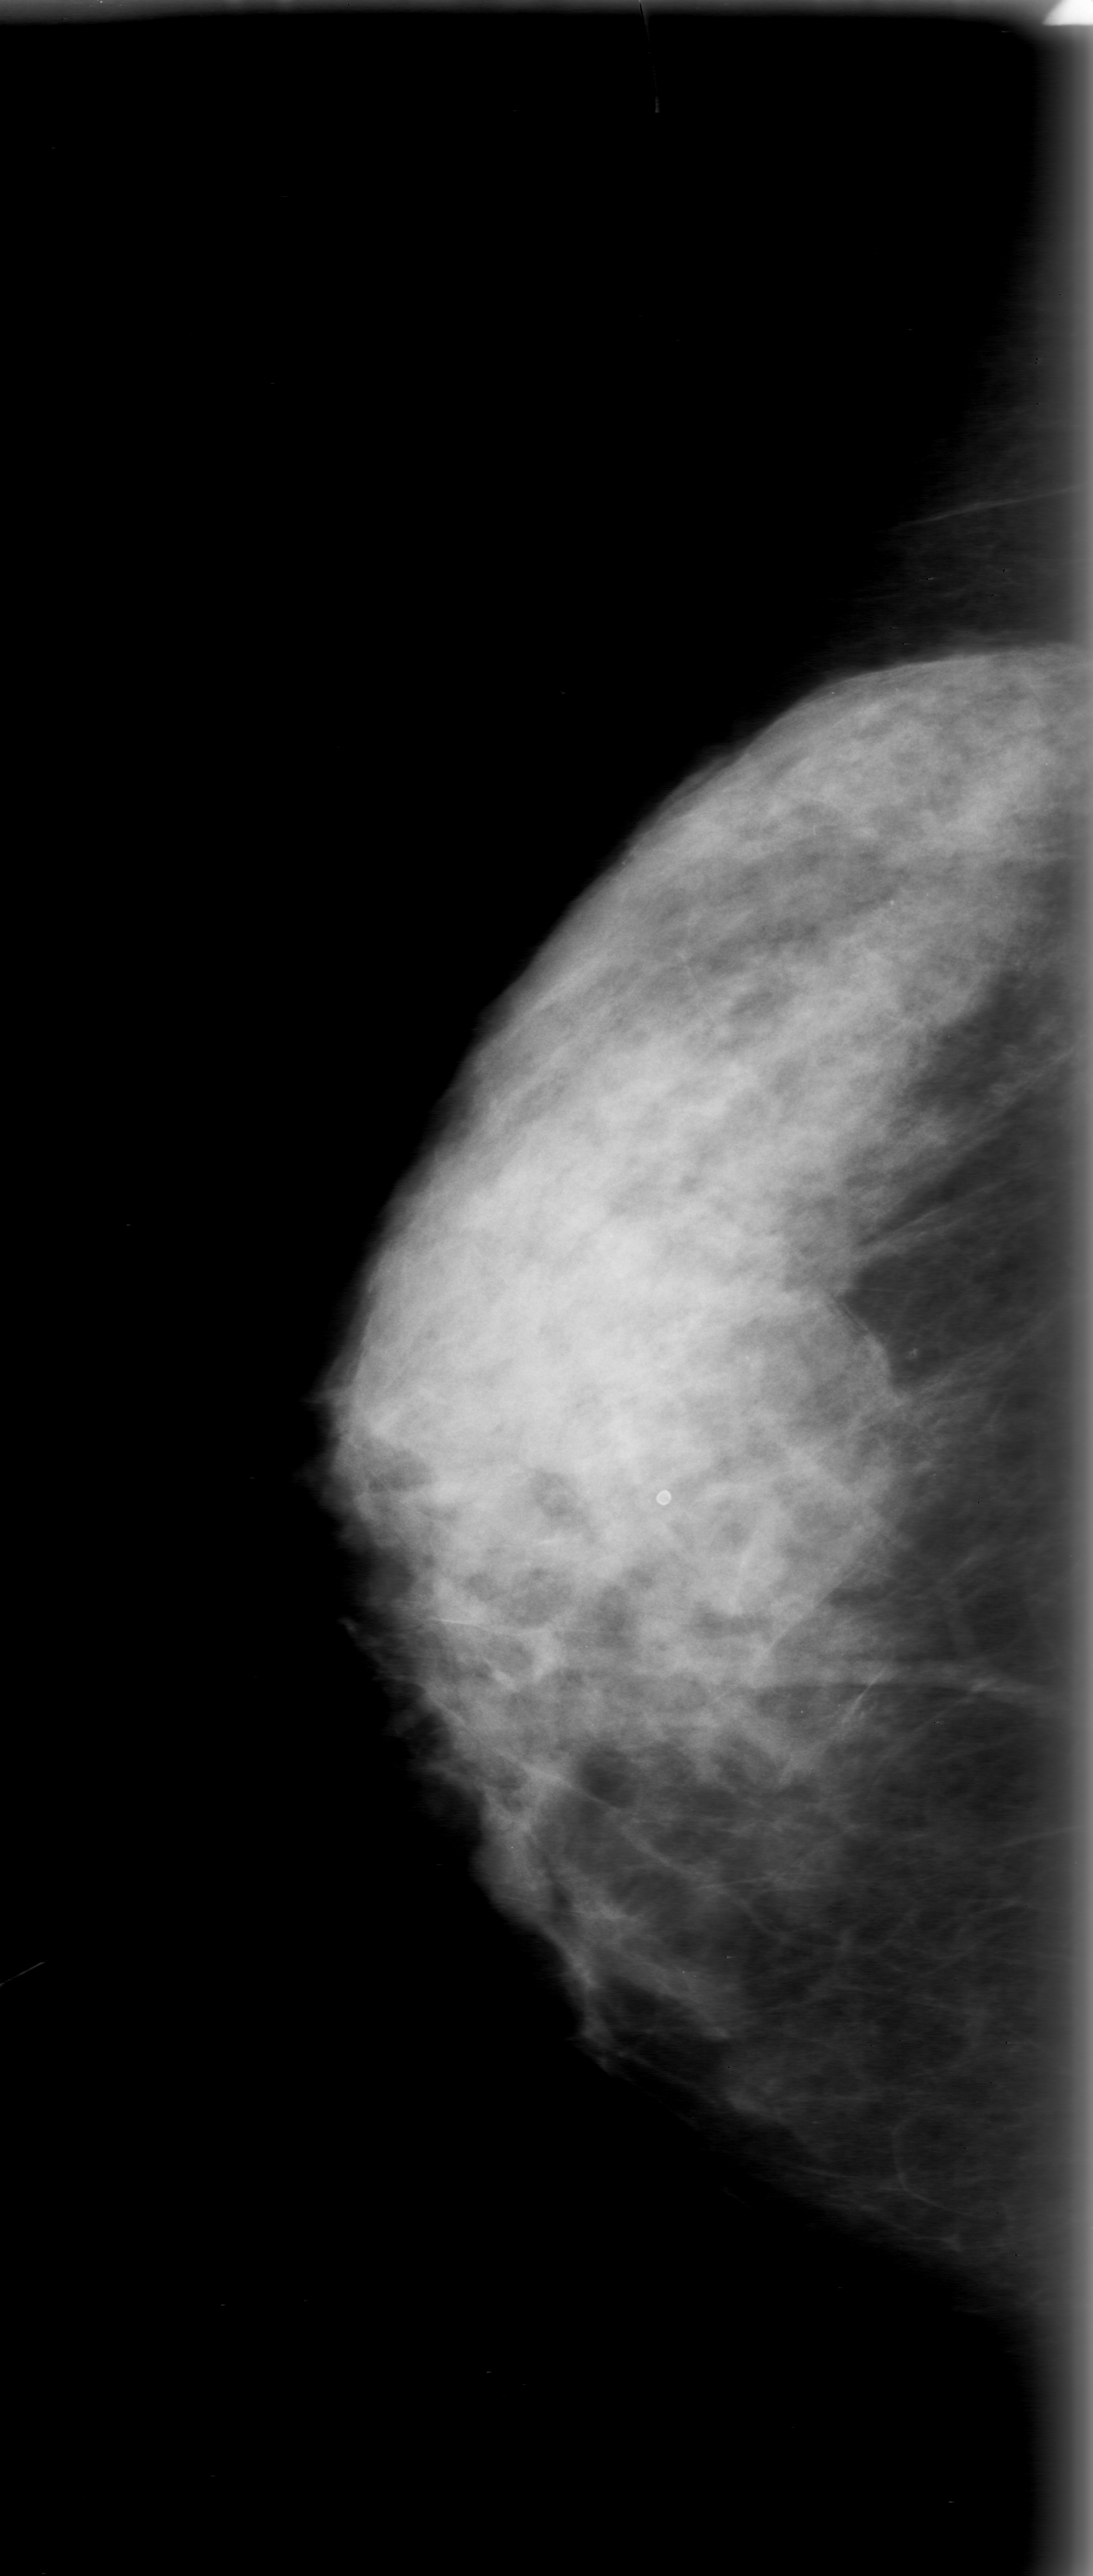
Scanned film-screen mammogram. Right breast. CC view. BI-RADS breast density category 4 (scale 1–4). 1093 × 2576 image matrix.
Marked abnormalities (boxes around the expert regions of interest):
- mass, shape lobulated, margins obscured; BI-RADS assessment category 0; subtlety rating 3 on a 1 (subtle) to 5 (obvious) scale; pathology result (as recorded, not read from the image): benign: bounding box <469,1836,560,1936> (left, top, right, bottom; pixels)